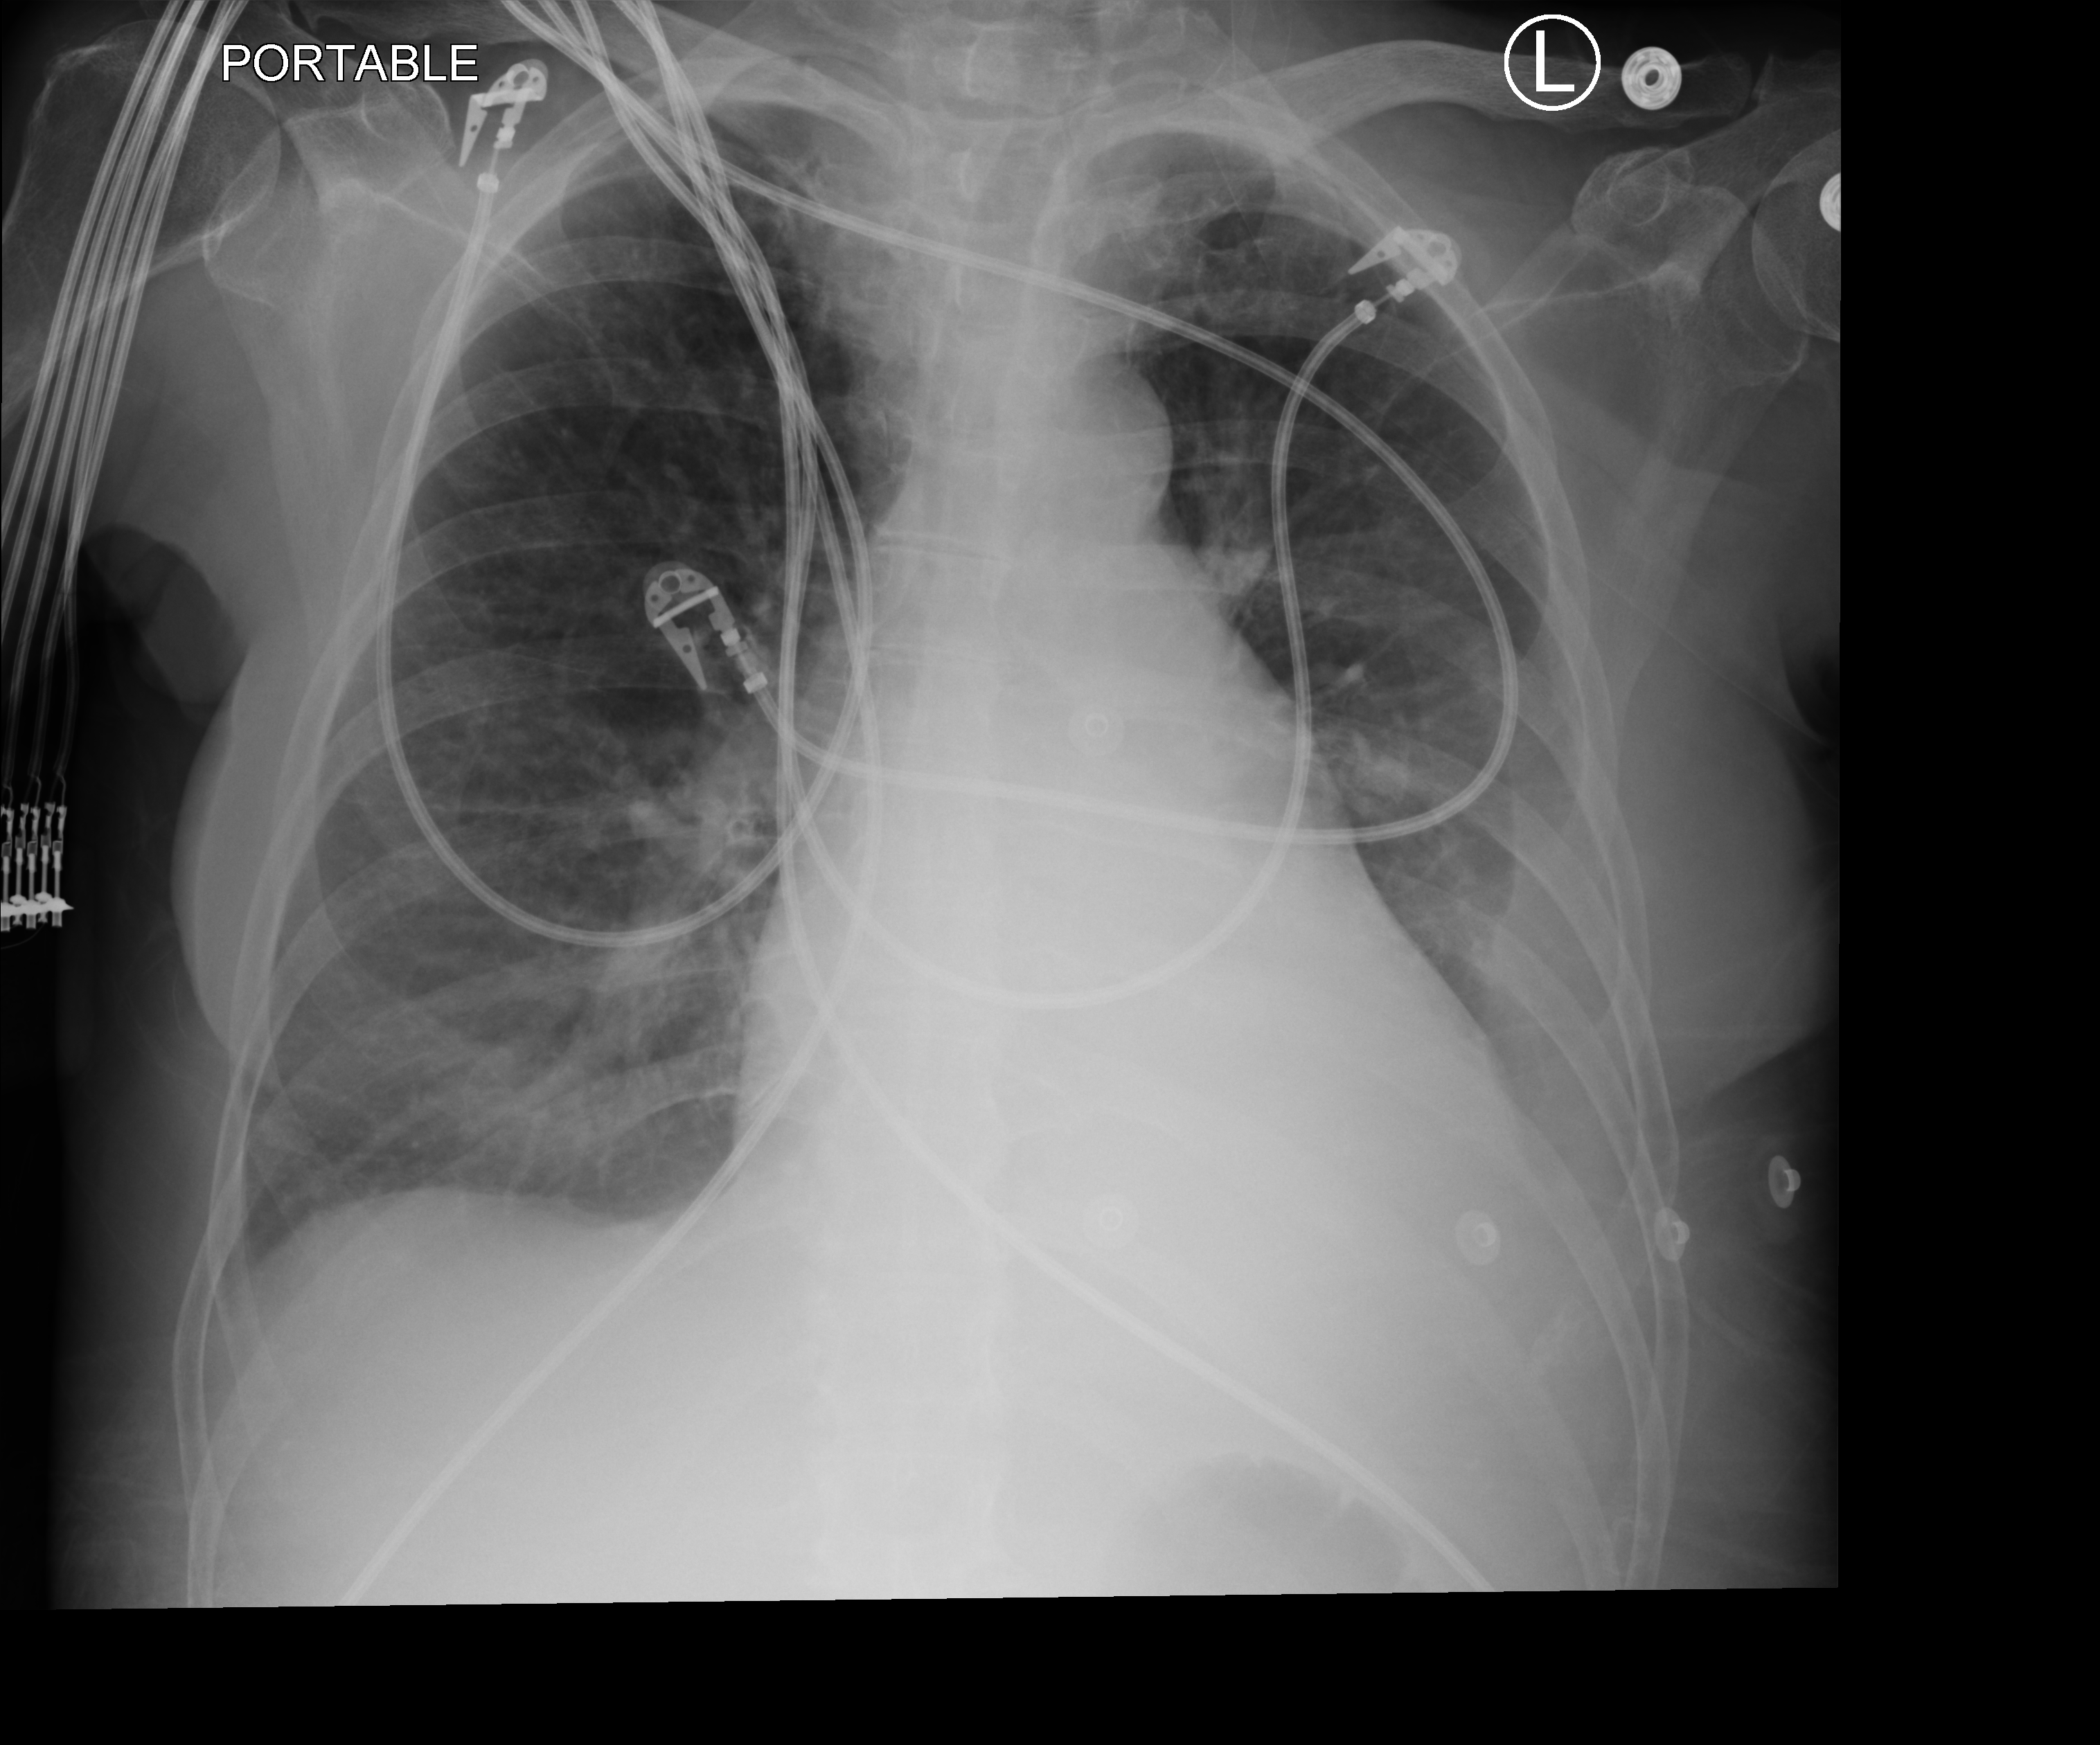
Bedside chest radiograph (computed radiography); anteroposterior (AP) projection. Patient hospitalised with COVID-19; female, aged 60–74 years.
Admission-level facts for this patient (not findings on this image; timing relative to this image not recorded): mechanically ventilated during this hospital stay: yes.